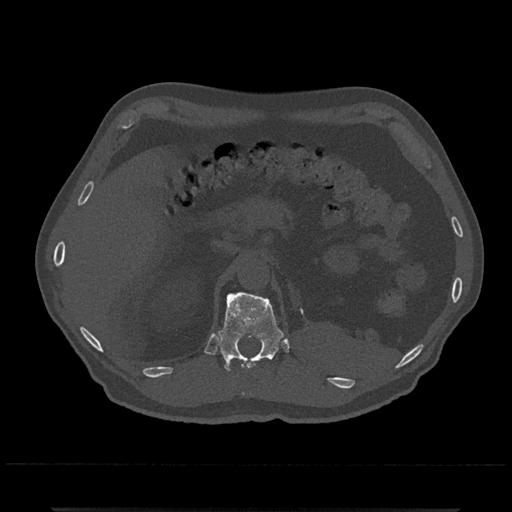
CT including the spine, one axial slice. Slice 441 of 797 in the series (ordered by position). Reconstruction kernel Br40s/3. 120 kVp. Bone window (W 1800 / L 400 HU). 512 × 512 image matrix, field of view 393 × 393 mm. Patient: male, 67 years. From the clinical record (not read from this slice): primary cancer: prostate.
Outlined on this slice (semi-automatic segmentation, software-assisted and operator-edited):
- T11 vertebra: bounding box (x1, y1, x2, y2) in pixels: (252, 361, 256, 365)
- T12 vertebra: (217, 292, 284, 373)